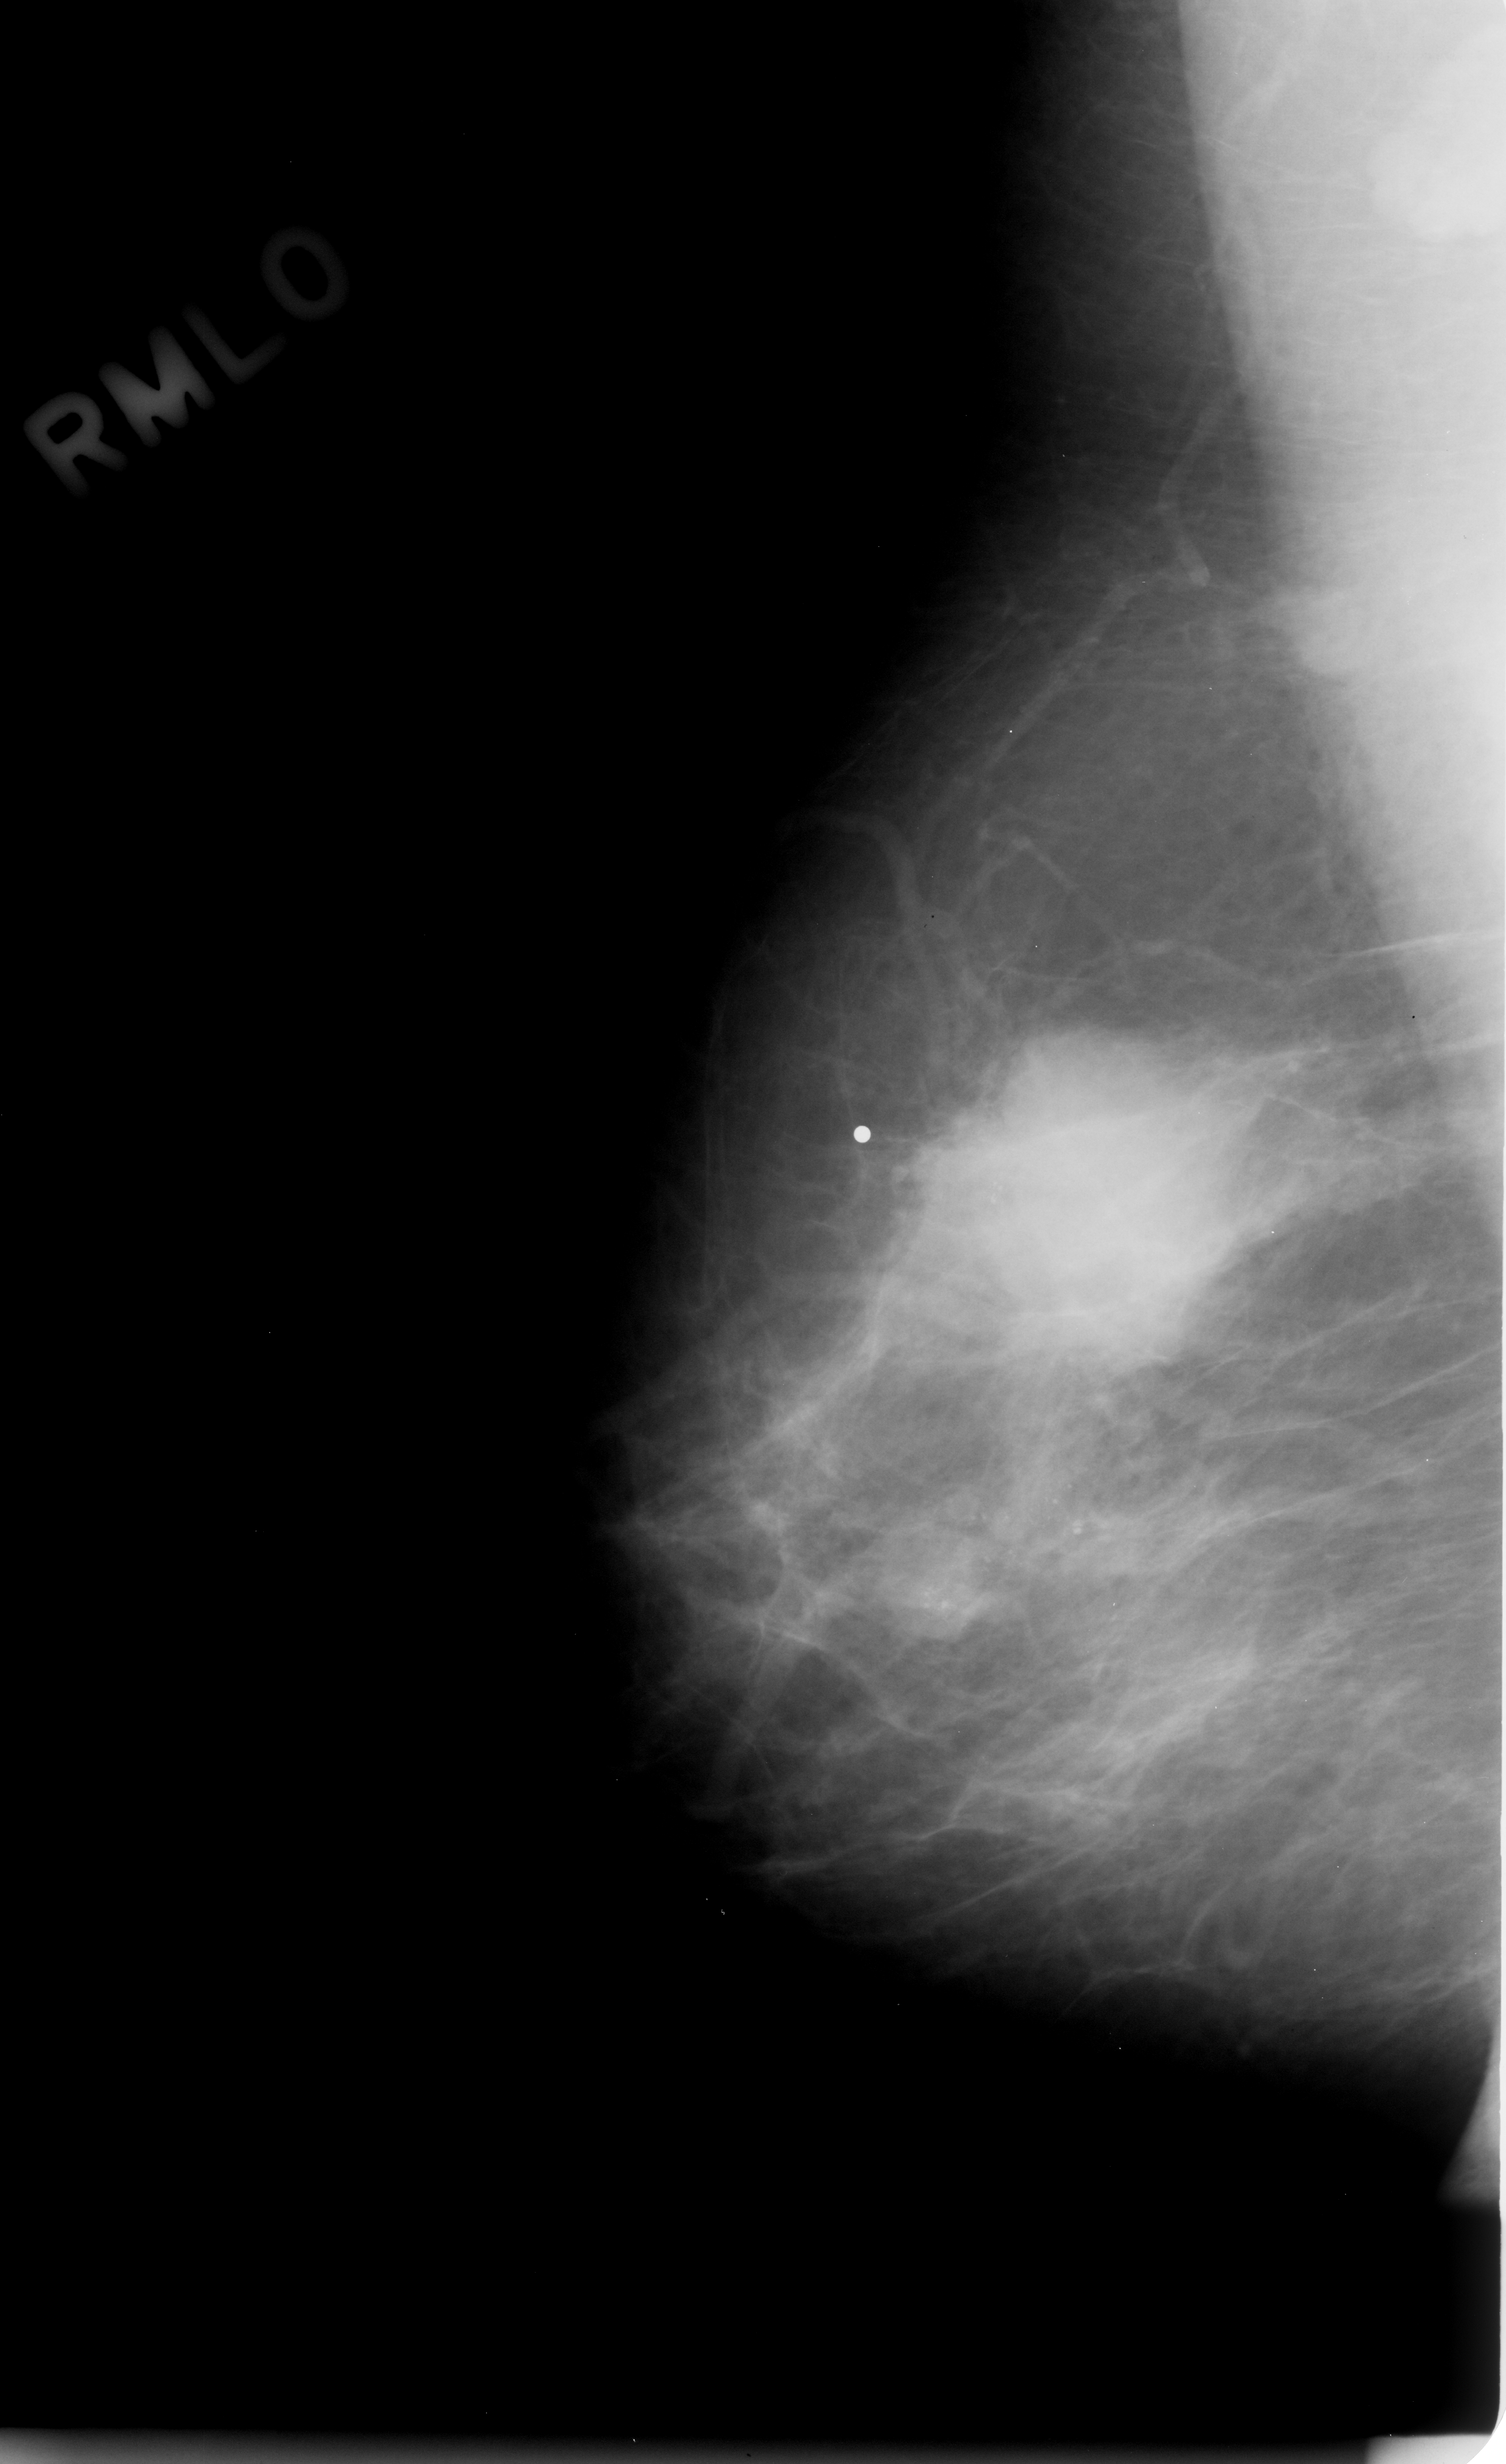
Digitized screen-film mammogram. Right breast. Mediolateral oblique (MLO) view. BI-RADS breast density category 1 (scale 1–4). 1506 × 2464 image matrix.
Expert-marked regions of interest on this image (one box per marked abnormality):
- calcifications, morphology amorphous, distribution clustered; BI-RADS assessment category 5; pathology result (as recorded, not read from the image): malignant: bounding box [x1, y1, x2, y2] px = [770, 842, 1486, 1720]